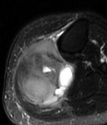
MRI of an extremity soft-tissue mass, one axial slice. Position 33 of 78 along the scan axis. T2-weighted fat-saturated. MR volume resampled by the dataset authors to the PET/CT grid (not the native acquisition matrix). 3.27 mm slice thickness. 107 × 125 image matrix, field of view 104 × 122 mm. Female patient. Case-level facts recorded for this patient, not image findings: histological type: extraskeletal high grade osteogenic sarcoma; grade: high; site of the primary tumour: left calf.
Structures marked on this image (expert contour drawn on MRI and transferred to this co-registered scan by the dataset authors):
- gross tumour volume (mass): bounding box [x1, y1, x2, y2] px = [17, 40, 72, 106]